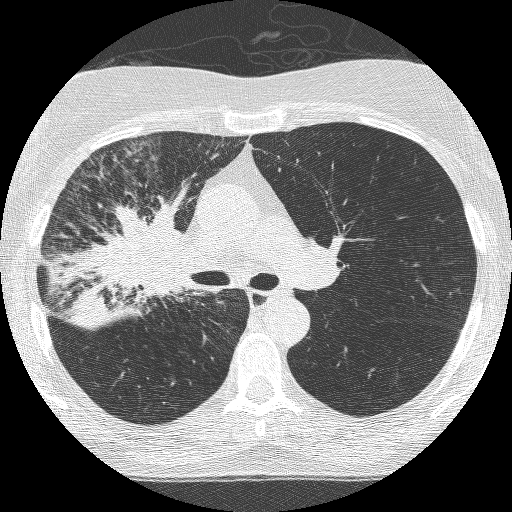
Low-dose screening chest CT, axial slice; third annual screen; lung window (W 1500 / L -600 HU); 1.25 mm slice thickness; lung (sharp) reconstruction kernel (BONE); slice 164 of 253 in the series. Female, age 64 years at enrolment. Former smoker at enrolment.
- Lesion marked by an expert reader, bounding box (x1, y1, x2, y2) in pixels: (81, 206, 204, 330).
- Screening reader's record for this exam (one nodule recorded; not confirmed to be the boxed lesion): non-calcified nodule or mass ≥4 mm, right upper lobe, 49 × 43 mm, spiculated (stellate) margins, soft tissue attenuation, pre-existing on the prior screen: yes; interval growth: yes.
- Participant outcome: lung cancer diagnosed 7 days after this screen — adenocarcinoma, NOS, right upper lobe, right middle lobe, right hilum, stage IV (AJCC 6th edition), 85 mm at pathology.